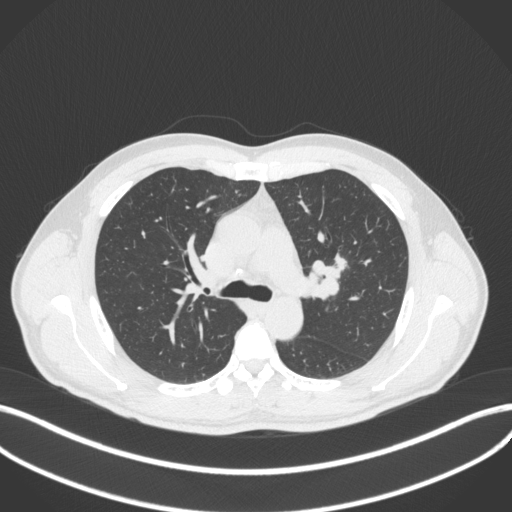
Chest CT, one axial slice; slice 277 of 383 in the series (ordered by position); reconstruction kernel B31f; 120 kVp; lung window (W 1500 / L -600 HU); 512 × 512 image matrix, field of view 400 × 400 mm. Patient: male, 50 years. From the clinical record (not read from this slice): clinical TNM (as recorded): T1c N1 M1b.
Structures marked on this image (rectangle marked by the reading radiologist):
- lung tumour (recorded histology: squamous cell carcinoma): bounding box (x1, y1, x2, y2) in pixels: (305, 250, 345, 302)